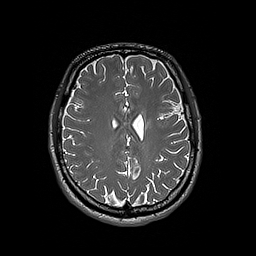
Brain MRI from a brain-tumour surgery series, one axial slice; position 71 of 192 along the scan axis; 1 mm slice thickness; 256 × 256 image matrix, field of view 250 × 250 mm. Case-level facts recorded for this patient, not image findings: histopathology: Oligodendroglioma; WHO grade: 3; IDH mutation: yes.
Outlined on this slice (outlined manually by an expert reader):
- tumour: bounding box (x1, y1, x2, y2) in pixels: (145, 120, 153, 129)